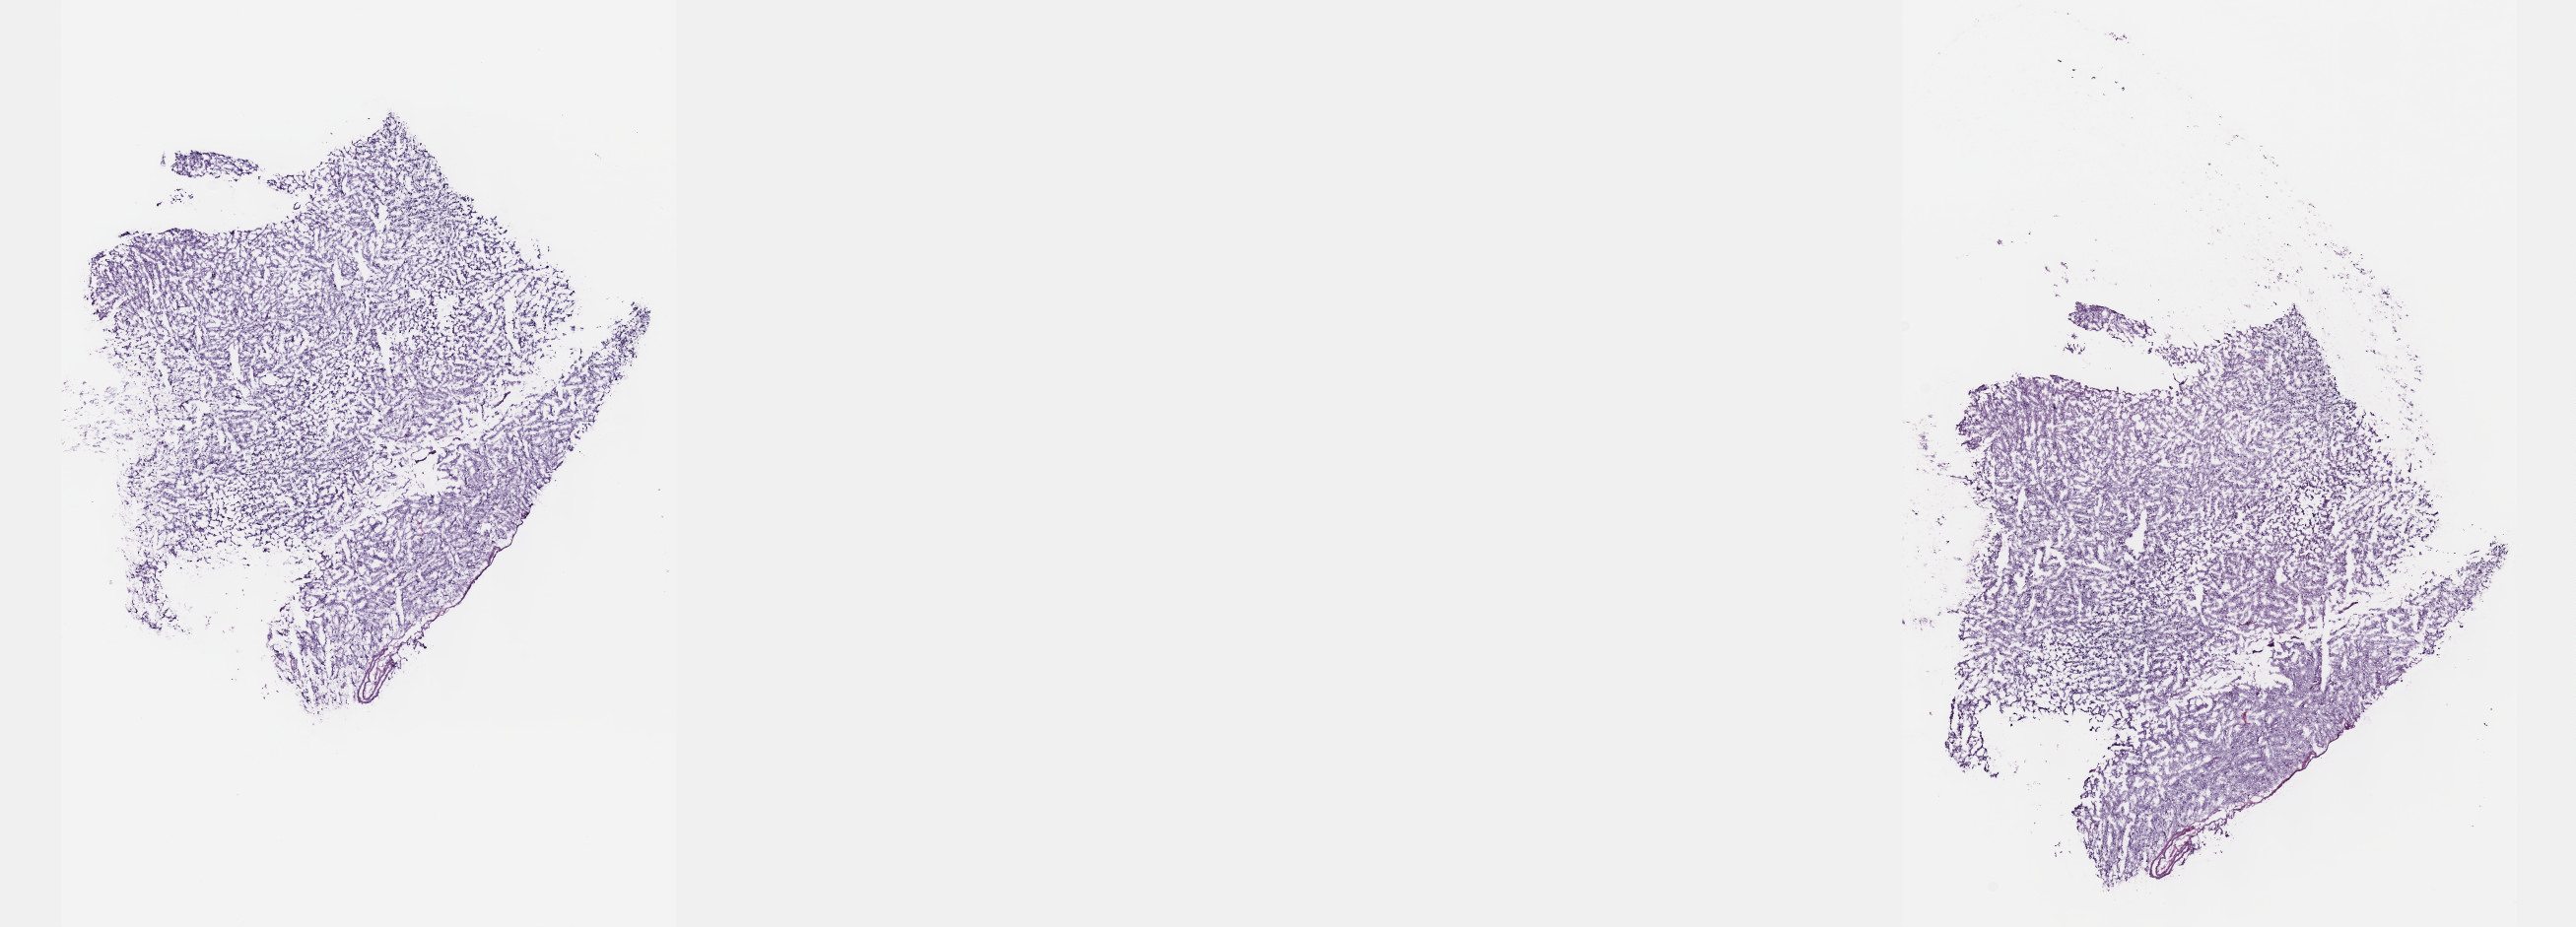
Whole-slide histology image, Hematoxylin and eosin (H&E) stained — whole scanned area (about 21.1 x 7.6 mm, slide scanned at 40x) shown as a low-resolution overview. Frozen section. Sample: primary tumour, brain. Patient: female, age at initial diagnosis 59 years.
Diagnosis: Oligodendroglioma, anaplastic (cerebrum).